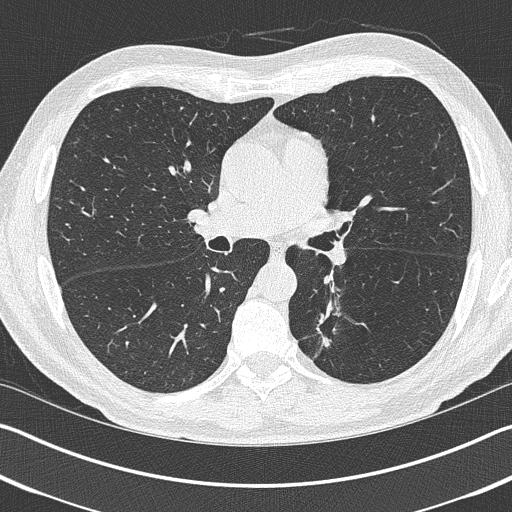
Low-dose screening chest CT, axial slice, first (baseline) screen, lung window (W 1500 / L -600 HU), 1 mm slice thickness. Male participant, aged 69 years at enrolment. Current smoker at enrolment.
Expert reader's lesion annotation, bounding box <298,307,354,361> (left, top, right, bottom; pixels). The exam's reader record, not a measurement of the box and not confirmed to be the same lesion: non-calcified nodule or mass ≥4 mm, left upper lobe, 19 × 19 mm, spiculated (stellate) margins, pre-existing on the prior screen: yes. Official screen result: positive, change unspecified: nodule(s) >= 4 mm or enlarging nodule(s), mass(es), or other non-specific abnormalities suspicious for lung cancer. Later outcome: lung cancer diagnosed 202 days after this screen — non-small cell carcinoma, left lower lobe, stage IIIA (AJCC 6th edition), 20 mm at pathology.